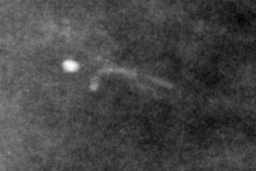
Region of interest cut from a scanned film mammogram (one marked finding); right breast; MLO view; BI-RADS breast density category 4 (scale 1–4).
Marked abnormality: calcifications, morphology fine linear branching, distribution linear; BI-RADS assessment category 4; subtlety rating 2 on a 1 (subtle) to 5 (obvious) scale; pathology (as recorded): malignant.